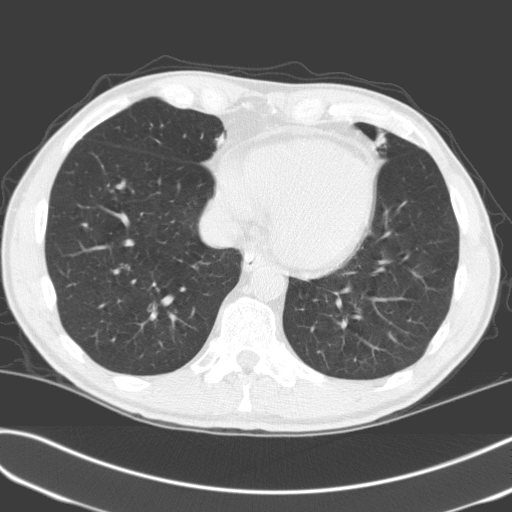
Low-dose screening chest CT, one axial slice; position 54 of 170 along the scan axis; lung window (W 1500 / L -600 HU); 3.2 mm slice thickness; 512 × 512 image matrix, field of view 351 × 351 mm.
Annotated regions visible in this slice (manually delineated by an expert):
- lesion 1 (tumor, upper lobe of left lung): box from (x=372, y=133) to (x=386, y=147) px